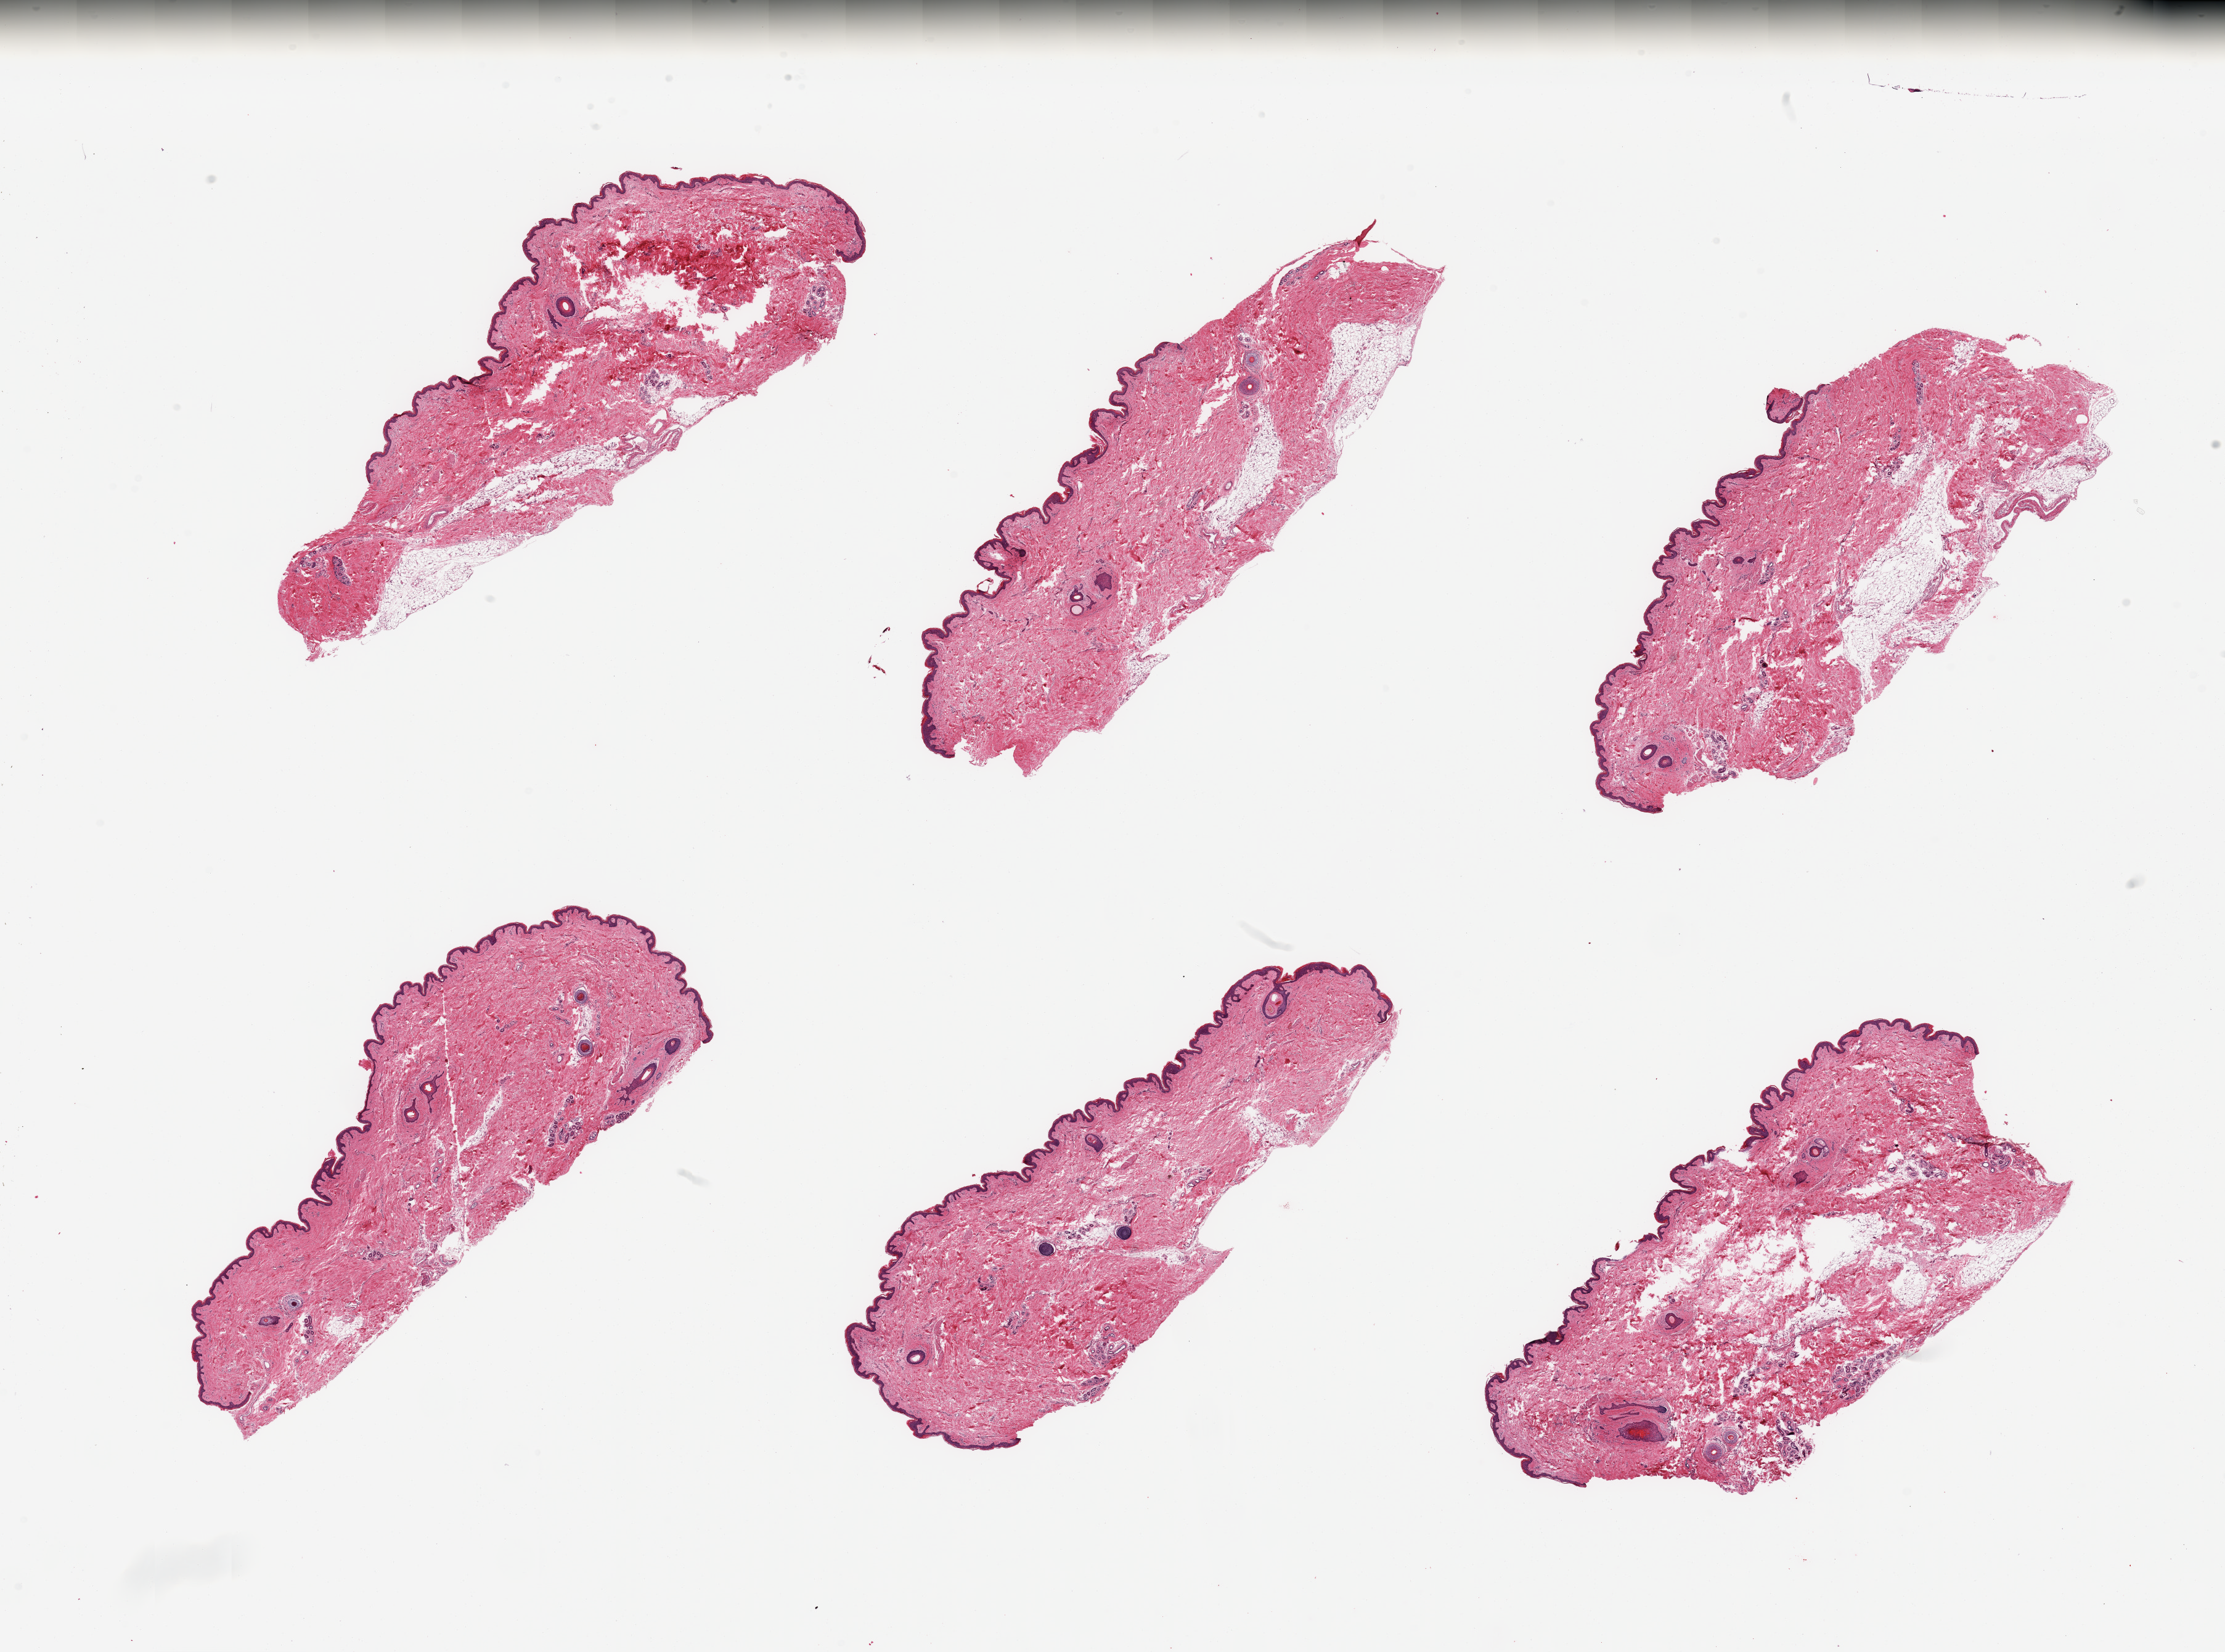
Hematoxylin and eosin (H&E) whole-slide image — low-resolution overview of the scanned area, about 28.5 x 21.2 mm (acquisition: 20x scan); PAXgene-fixed, paraffin-embedded tissue; target tissue: skin of suprapubic region; tissue donor sample. Male donor.
Pathologist's review note for this sample: 6 pieces; hair bearing skin with 5% to 30% internal/external fat.